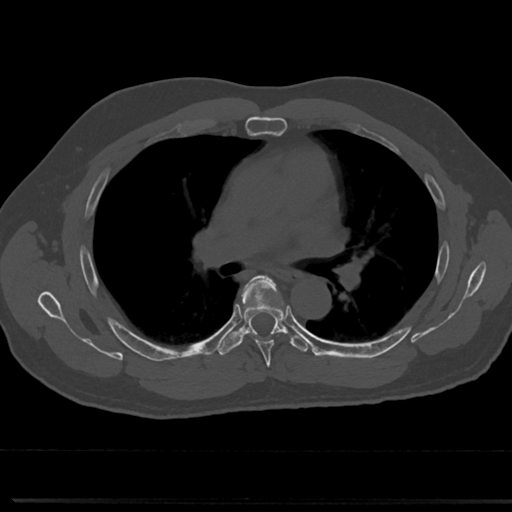
CT including the spine, one axial slice; slice 474 of 817 in the series (ordered by position); bone window (W 1800 / L 400 HU); 0.5 mm slice thickness; 512 × 512 image matrix, field of view 355 × 355 mm. Patient: male, 61 years. Case-level facts recorded for this patient, not image findings: primary cancer: prostate.
Annotated regions visible in this slice (semi-automatically segmented with operator editing):
- T5 vertebra: bounding box [x1, y1, x2, y2] px = [239, 277, 288, 360]
- T6 vertebra: [222, 323, 287, 350]